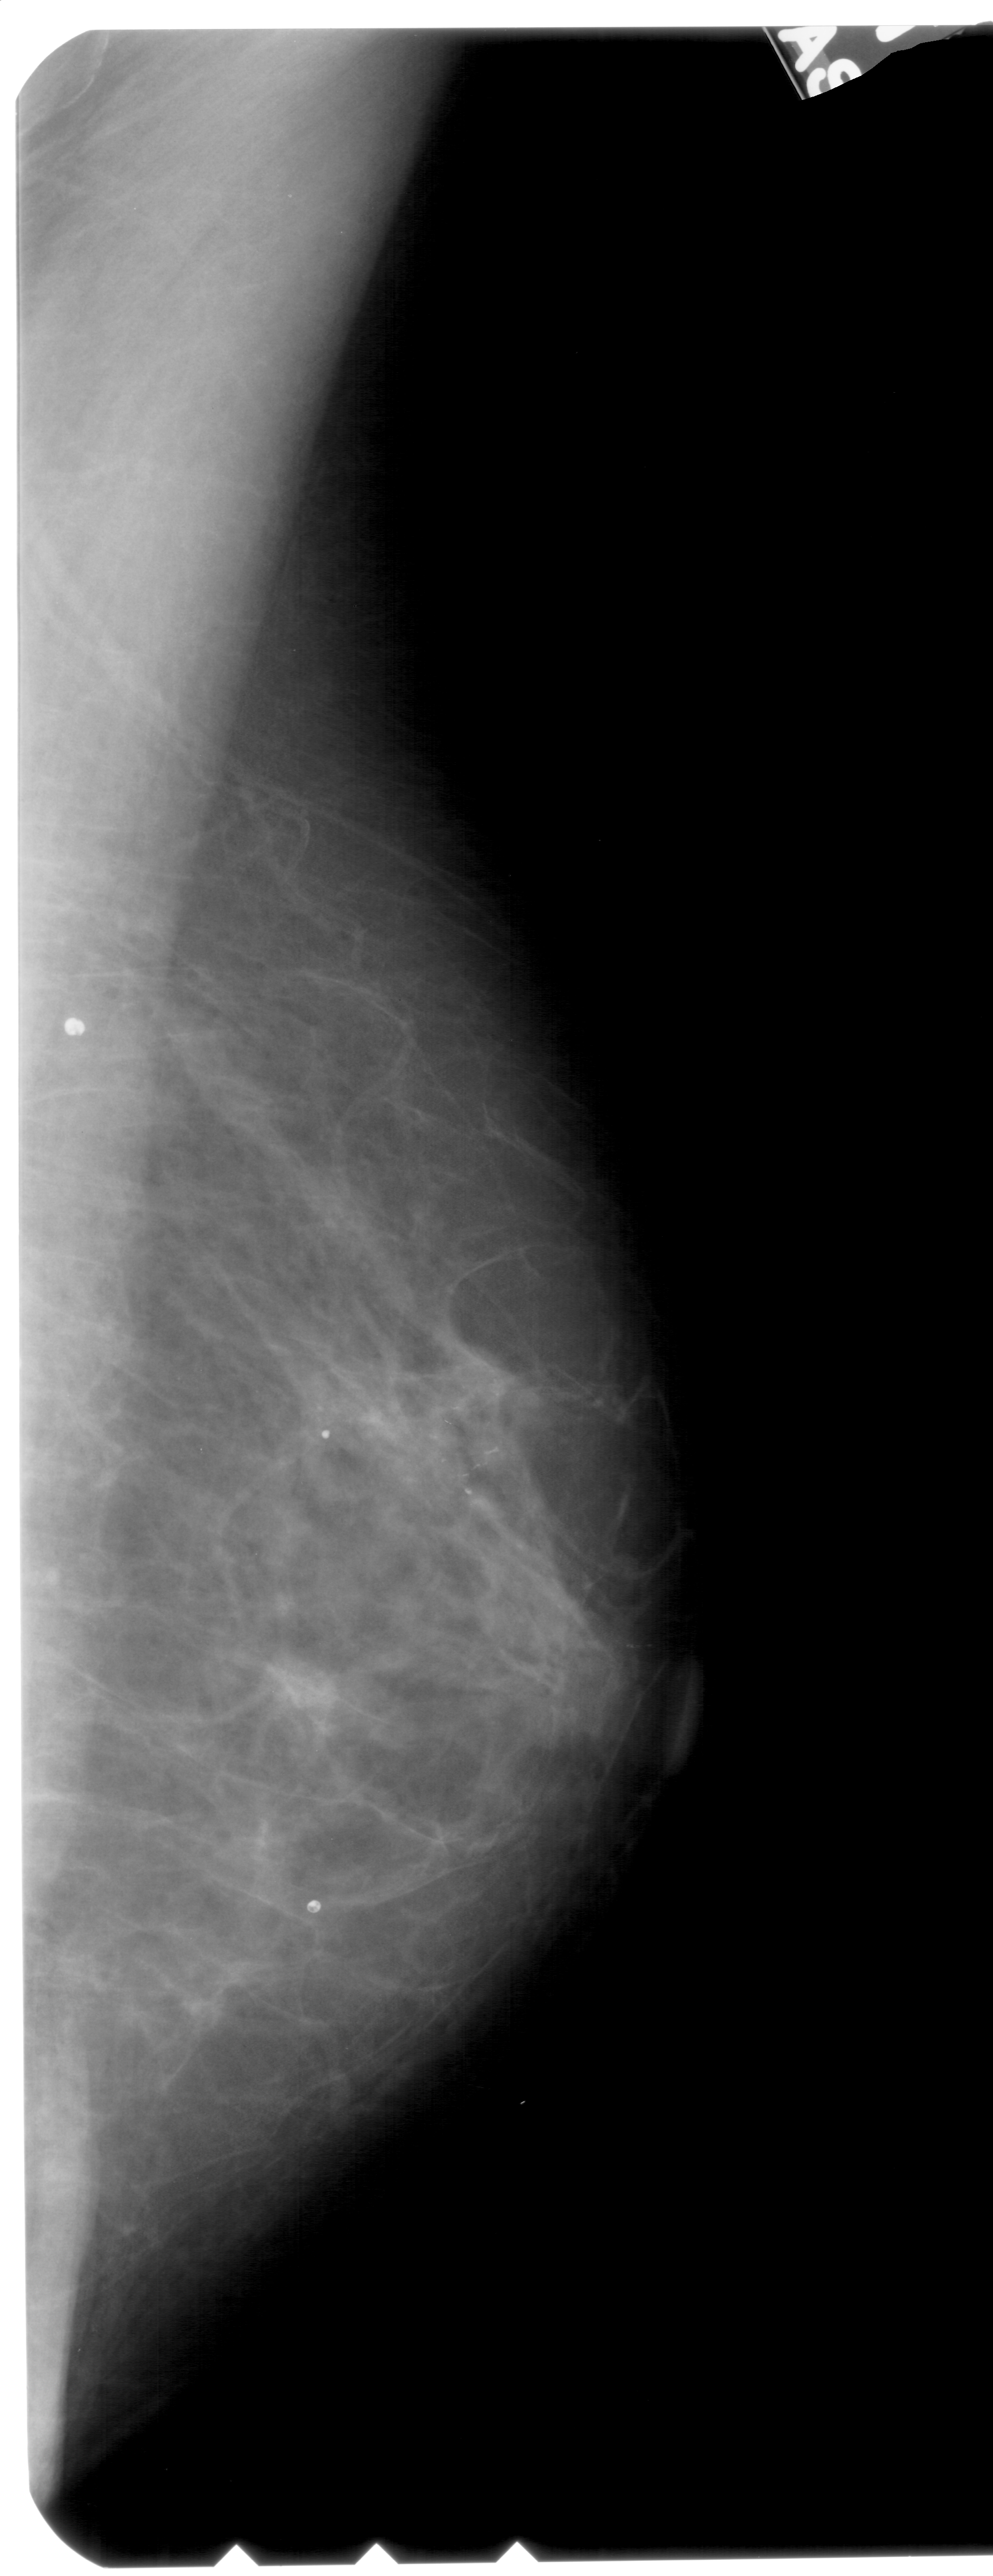
Digitized screen-film mammogram; right breast; mediolateral oblique (MLO) view; breast composition: scattered fibroglandular densities (BI-RADS density category 2 of 4); 993 × 2576 image matrix.
Marked abnormalities (boxes around the expert regions of interest):
- calcifications, morphology pleomorphic, distribution clustered; BI-RADS assessment category 4; subtlety rating 2 on a 1 (subtle) to 5 (obvious) scale; pathology (as recorded): malignant: bounding box (x1, y1, x2, y2) in pixels: (422, 1375, 521, 1493)